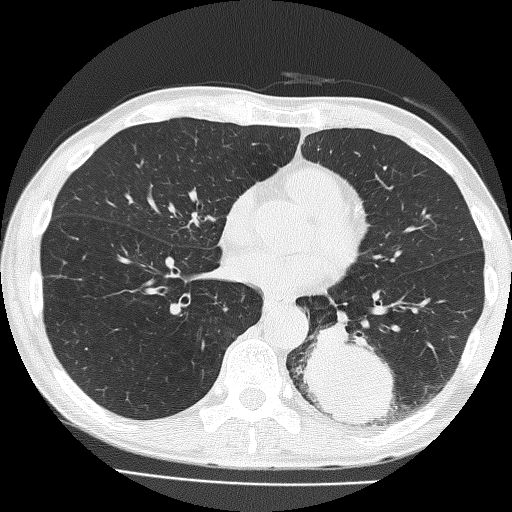
Low-dose screening chest CT, axial slice, baseline annual screen, lung window (W 1500 / L -600 HU), 2 mm slice thickness, lung (sharp) reconstruction kernel (FC51), slice 89 of 160 in the series. Male participant, aged 58 years at enrolment. Current smoker at enrolment.
- 2 expert reader's lesion annotations on this slice (largest first), bounding box (x1, y1, x2, y2) in pixels: (300, 310, 420, 434); (292, 321, 410, 434).
- The screening reader recorded 2 non-calcified nodules or masses ≥4 mm on this exam; which of them these boxes mark is not recorded.
- Later outcome: lung cancer diagnosed 39 days after this screen — non-small cell carcinoma, left lower lobe, poorly differentiated (G3), stage IV (AJCC 6th edition), 74 mm at pathology.